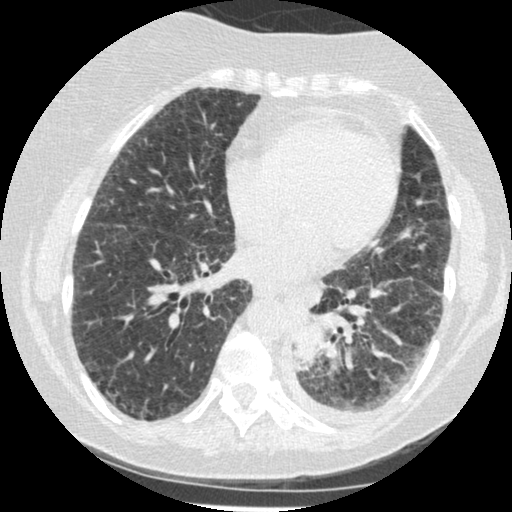
Chest CT (low-dose screening protocol), one axial image. Third annual screen. Lung window (W 1500 / L -600 HU). Female participant, aged 60 years at enrolment. Former smoker at enrolment.
Expert reader's lesion annotation, bounding box (x1, y1, x2, y2) in pixels: (279, 301, 344, 376). The exam's reader record, not a measurement of the box and not confirmed to be the same lesion: non-calcified nodule or mass ≥4 mm, left lower lobe, 54 × 38 mm, smooth margins, soft tissue attenuation, pre-existing on the prior screen: yes; interval growth: yes. Later outcome: lung cancer diagnosed 15 days after this screen — small cell carcinoma, NOS, left lower lobe, undifferentiated (G4), stage IV (AJCC 6th edition), 69 mm at pathology.